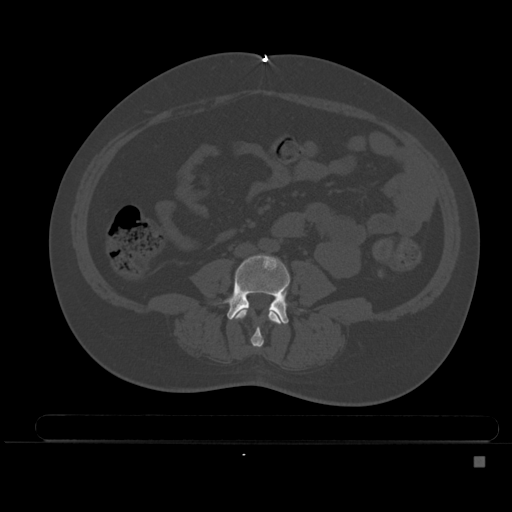
CT including the spine, one axial slice; bone window (W 1800 / L 400 HU); 1.5 mm slice thickness; 512 × 512 image matrix, field of view 404 × 404 mm. Female patient, age 33 years. Case-level facts recorded for this patient, not image findings: primary cancer: breast; vertebrae with lytic lesions (as recorded): T1.
Outlined on this slice (semi-automatically segmented with operator editing):
- L3 vertebra: bounding box [x1, y1, x2, y2] px = [234, 308, 284, 348]
- L4 vertebra: [227, 253, 290, 324]